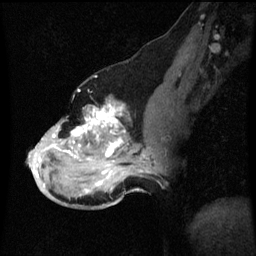
Breast MRI (dynamic contrast-enhanced), one sagittal slice. Slice 31 of 60 in the series (ordered by position). Dynamic contrast-enhanced series, image 2 of 3 at this slice position (ordered by acquisition). 1.5 T. TE 4.2 ms, TR 8.9 ms. 2 mm slice thickness. 256 × 256 image matrix, field of view 200 × 200 mm. Patient: female, 49 years. From the clinical record (not read from this slice): setting: breast cancer imaged before/during neoadjuvant chemotherapy; receptor status: HR-positive, HER2-negative.
Outlined on this slice (semi-automatic segmentation, software-assisted and operator-edited):
- analysis volume of interest (the breast-tissue region the enhancement analysis was run in; not a lesion): bounding box (x1, y1, x2, y2) in pixels: (30, 100, 159, 199)
- tumour enhancement mask (voxels above the 70 % enhancement threshold inside the analysis volume of interest): (36, 104, 149, 191)